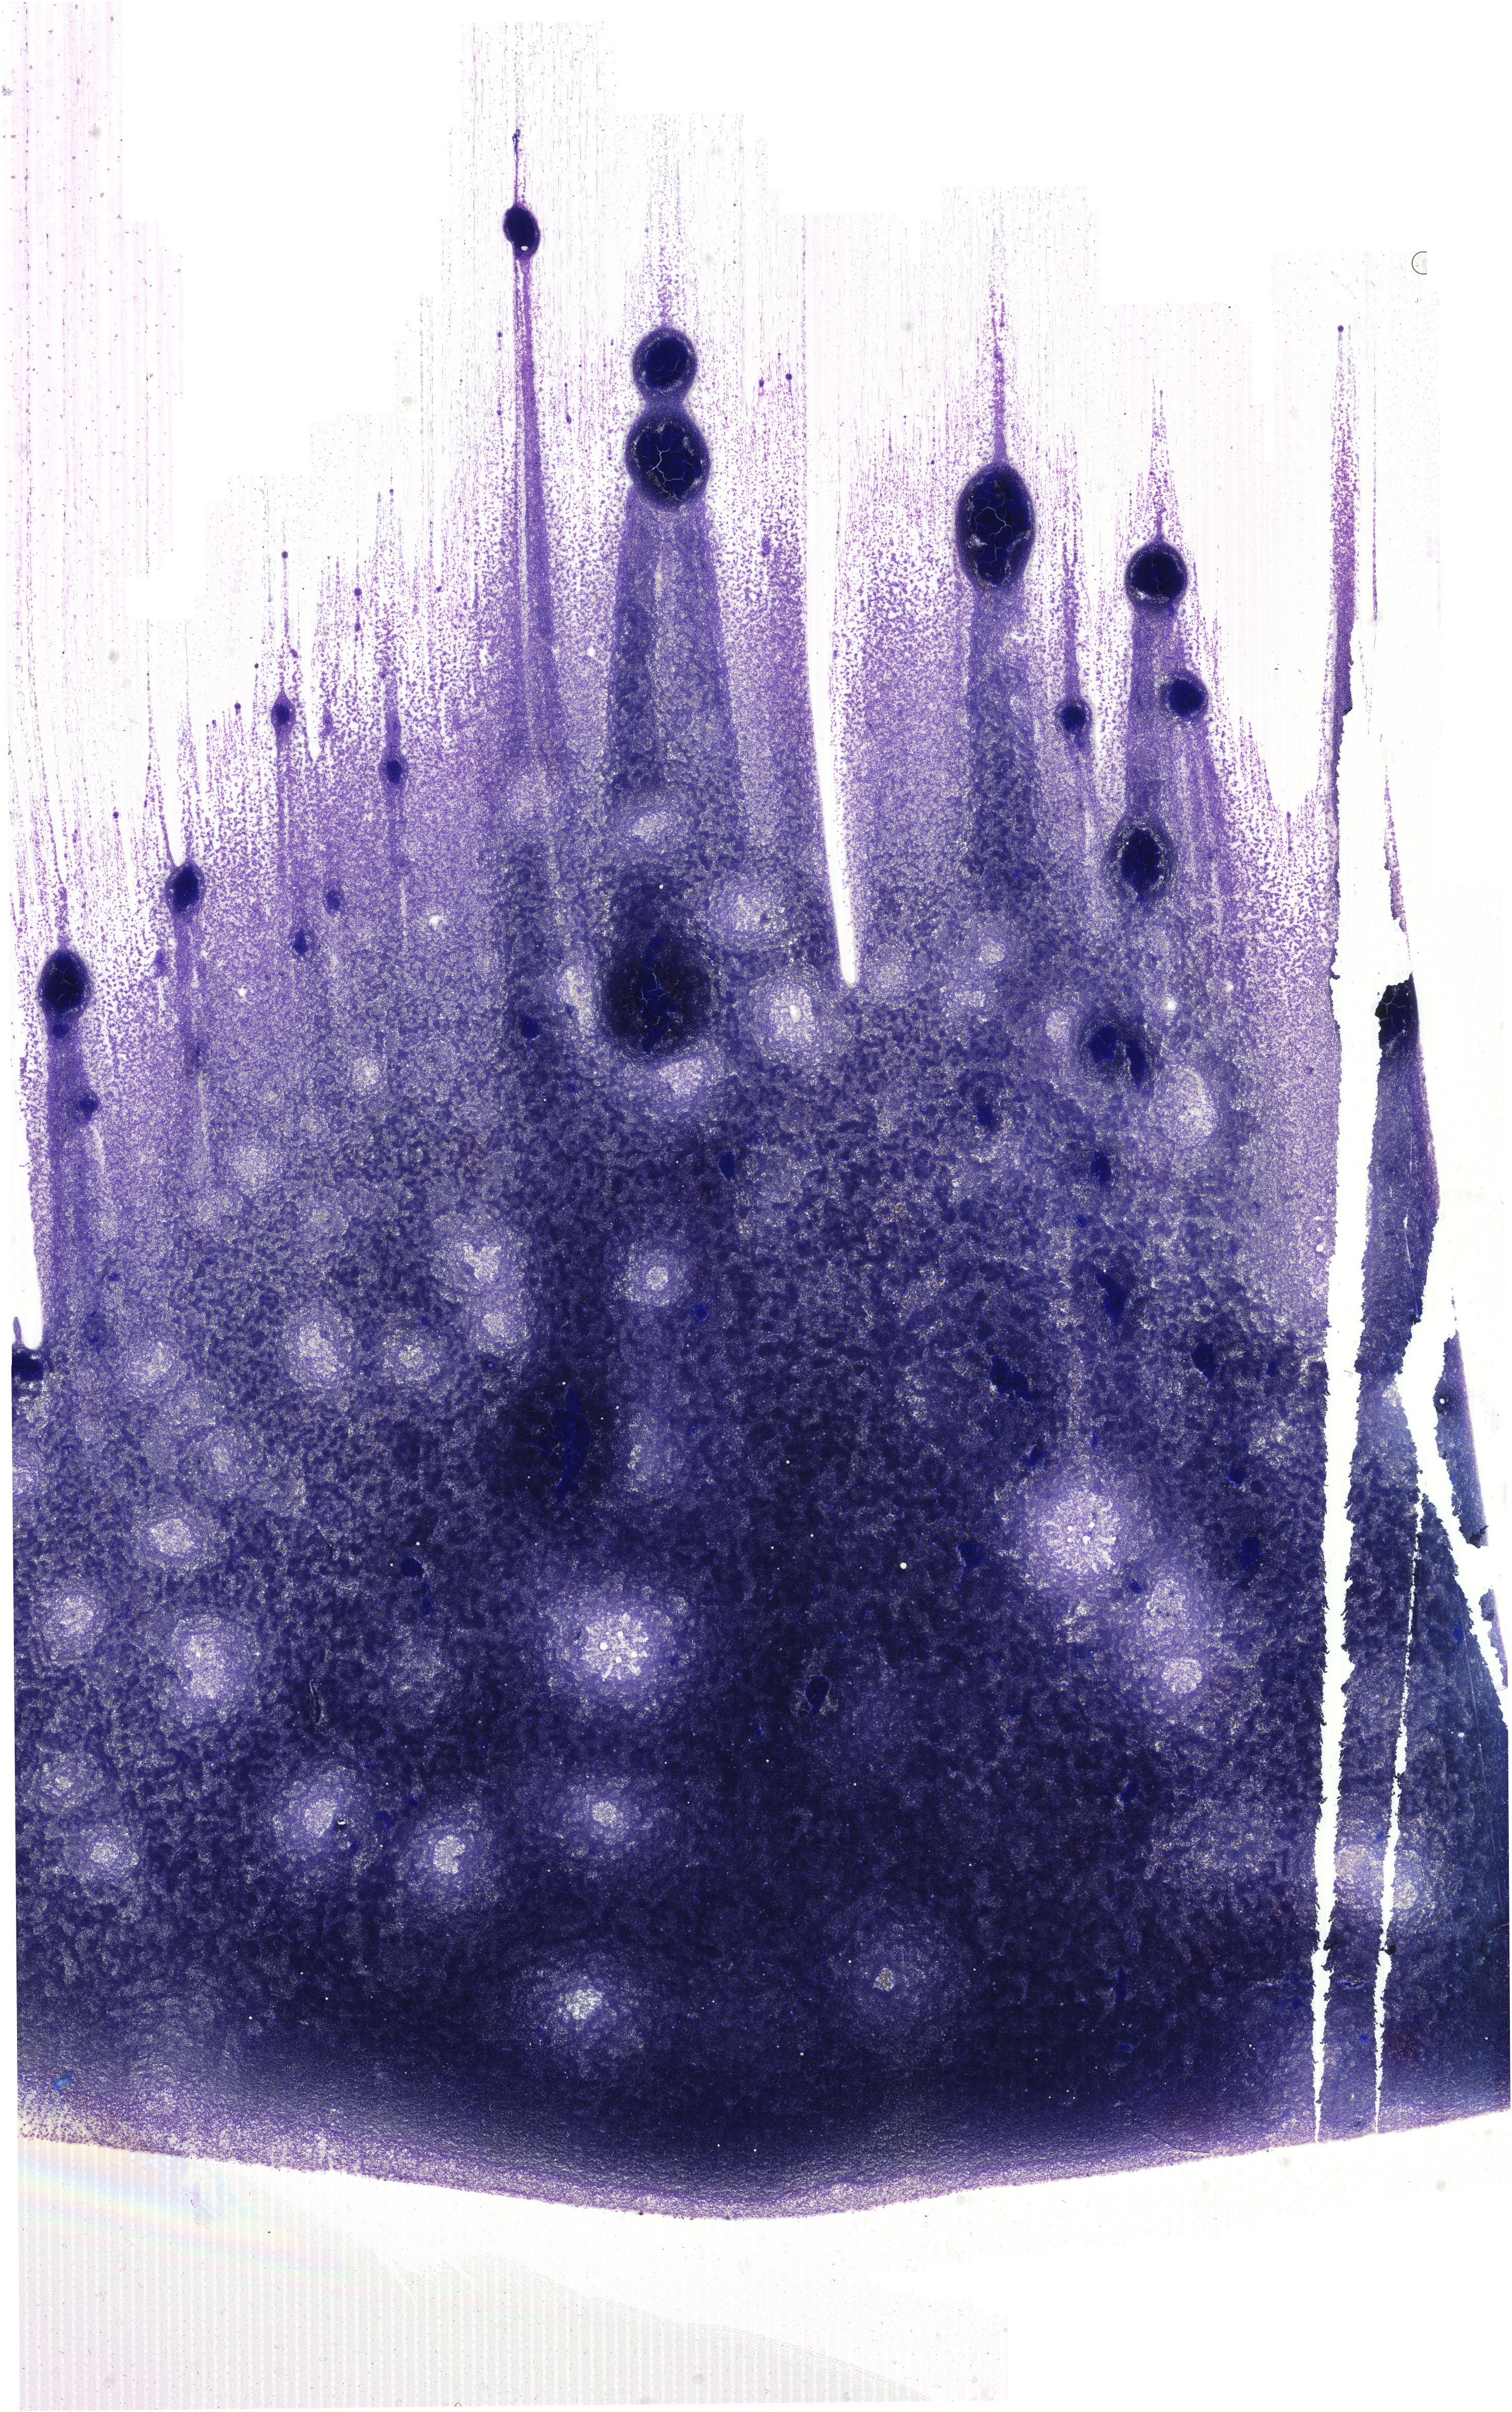
Bone marrow aspirate smear, May-Grünwald-Giemsa (MGG) stain, whole-slide image, low-resolution overview of the scanned area, about 20.8 x 33.1 mm. Patient sex: female.
Diagnosis: Chronic Phase Chronic Myeloid Leukemia, BCR-ABL1 Positive.